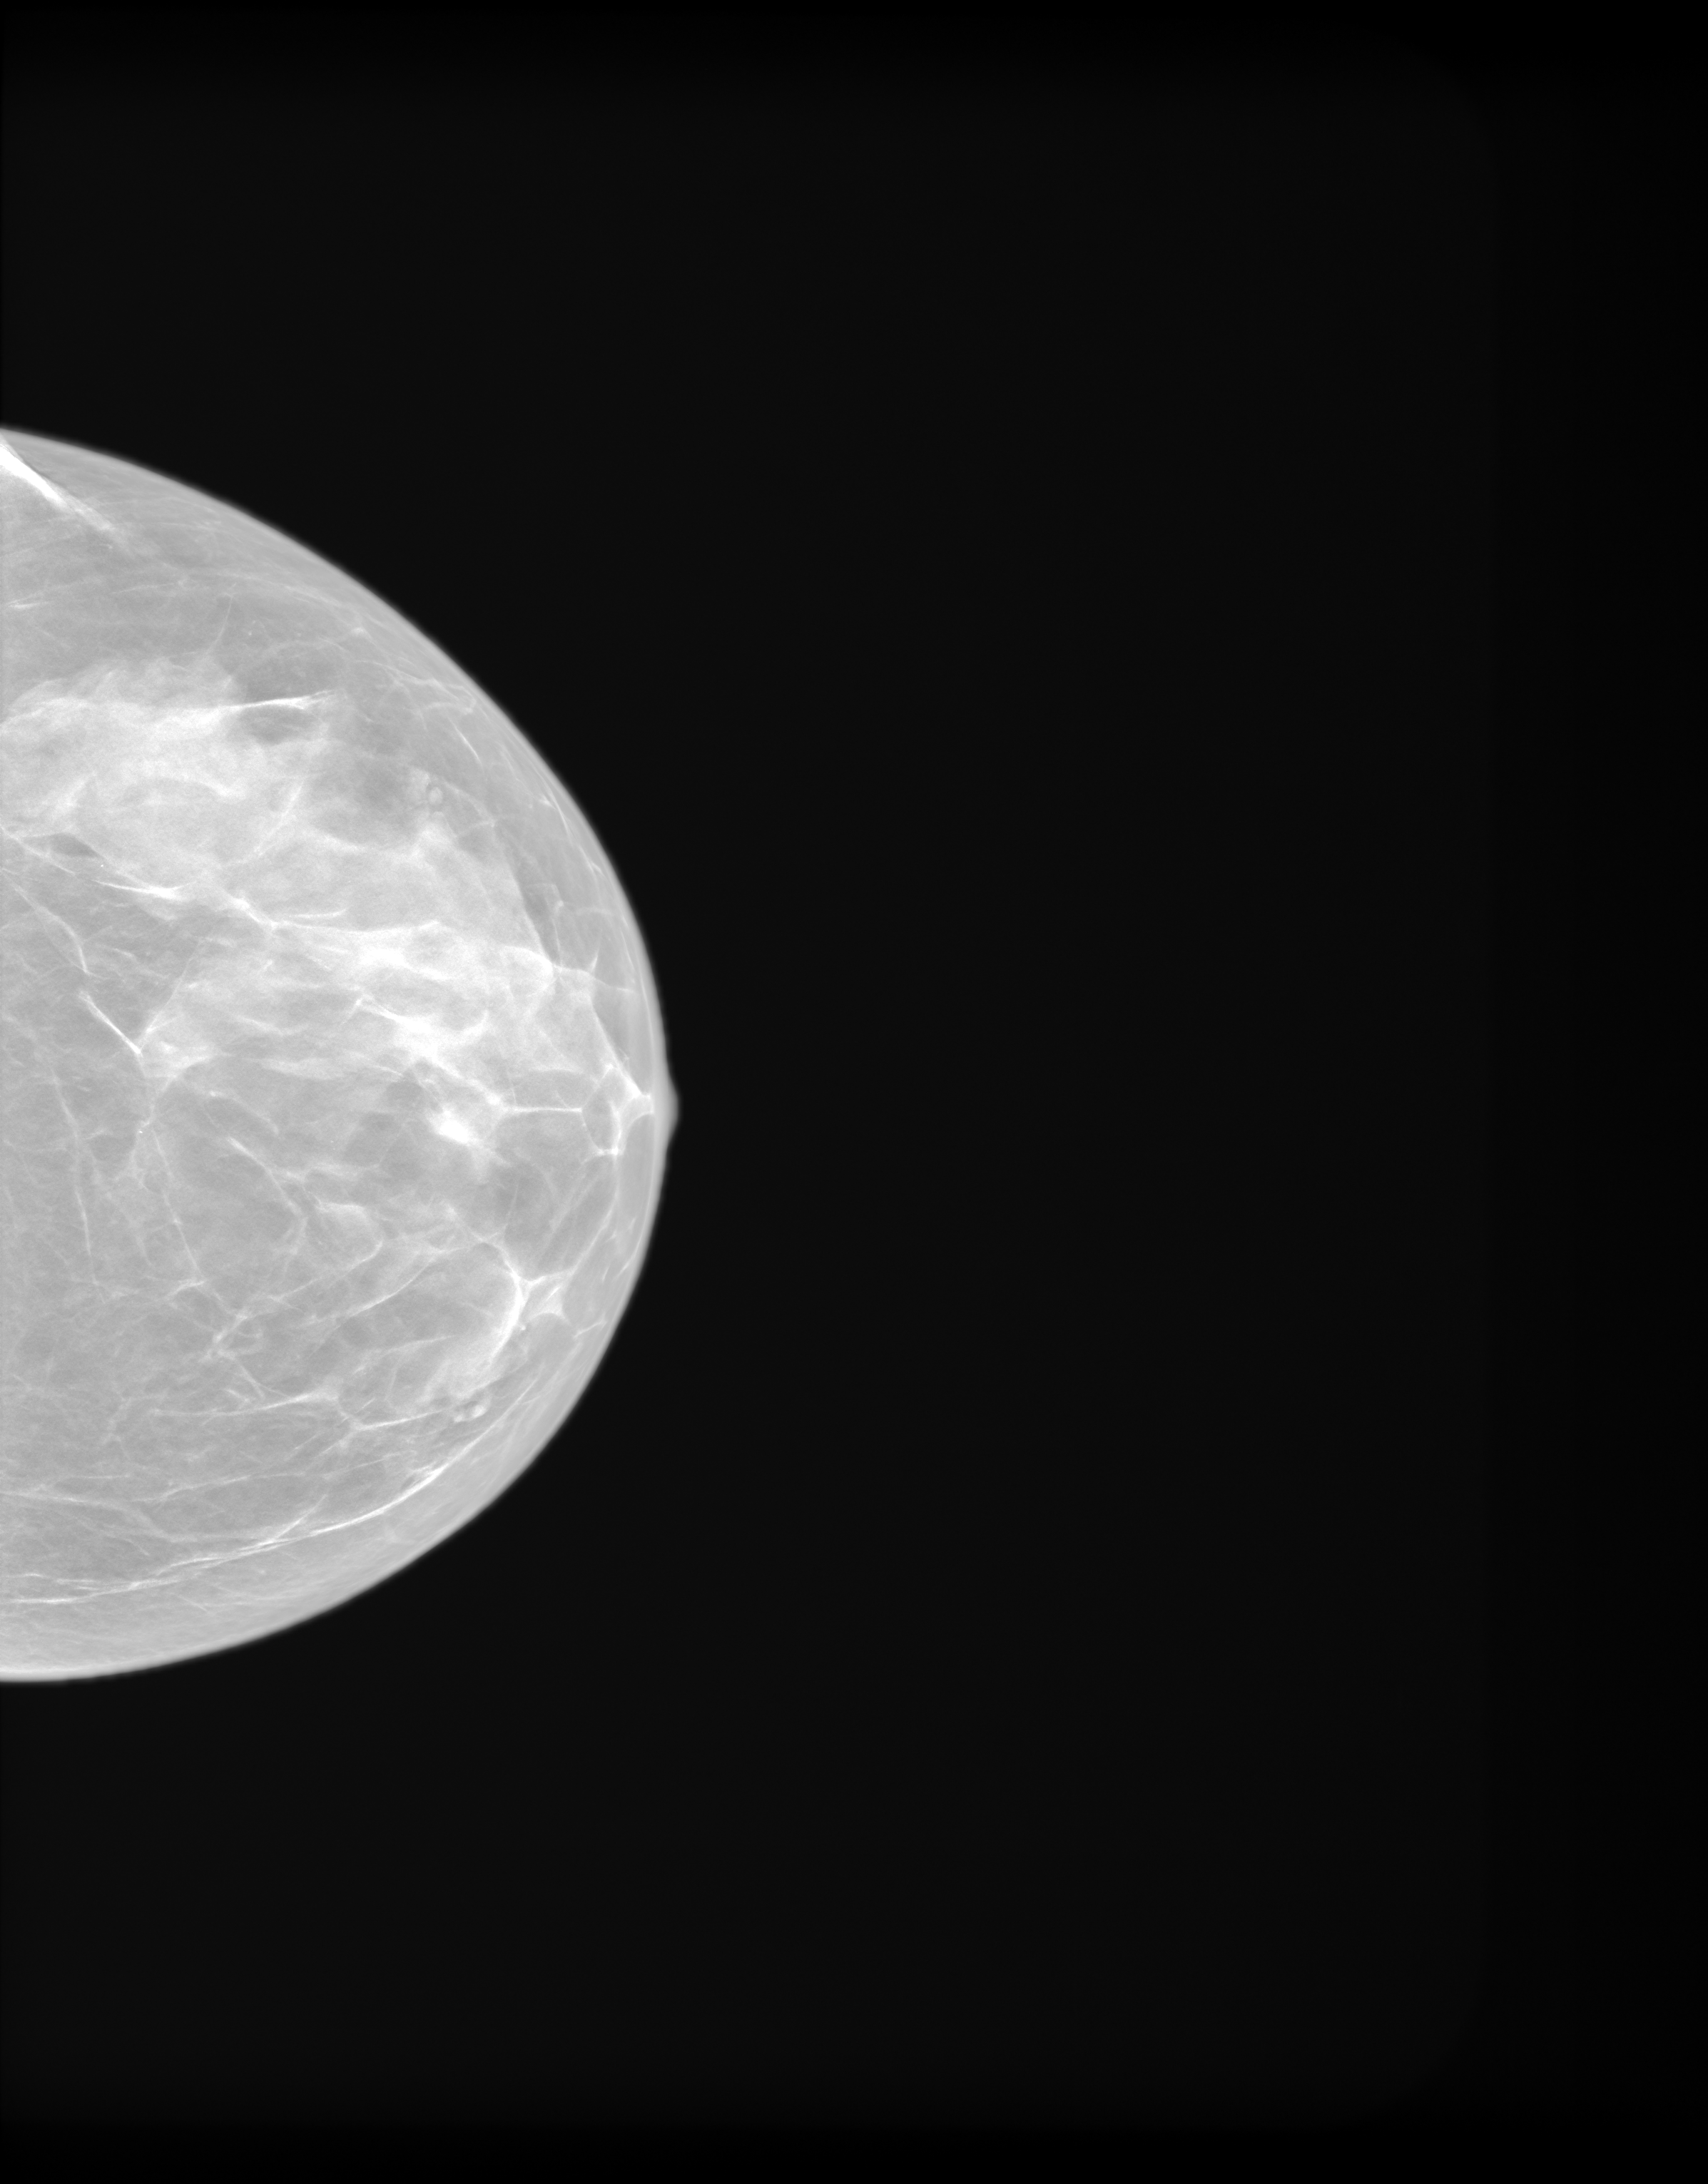
Annual screening mammography examination. Patient: female, 52 years.
Image type: synthesized 2-D view from tomosynthesis. Breast: left. Projection: CC view.